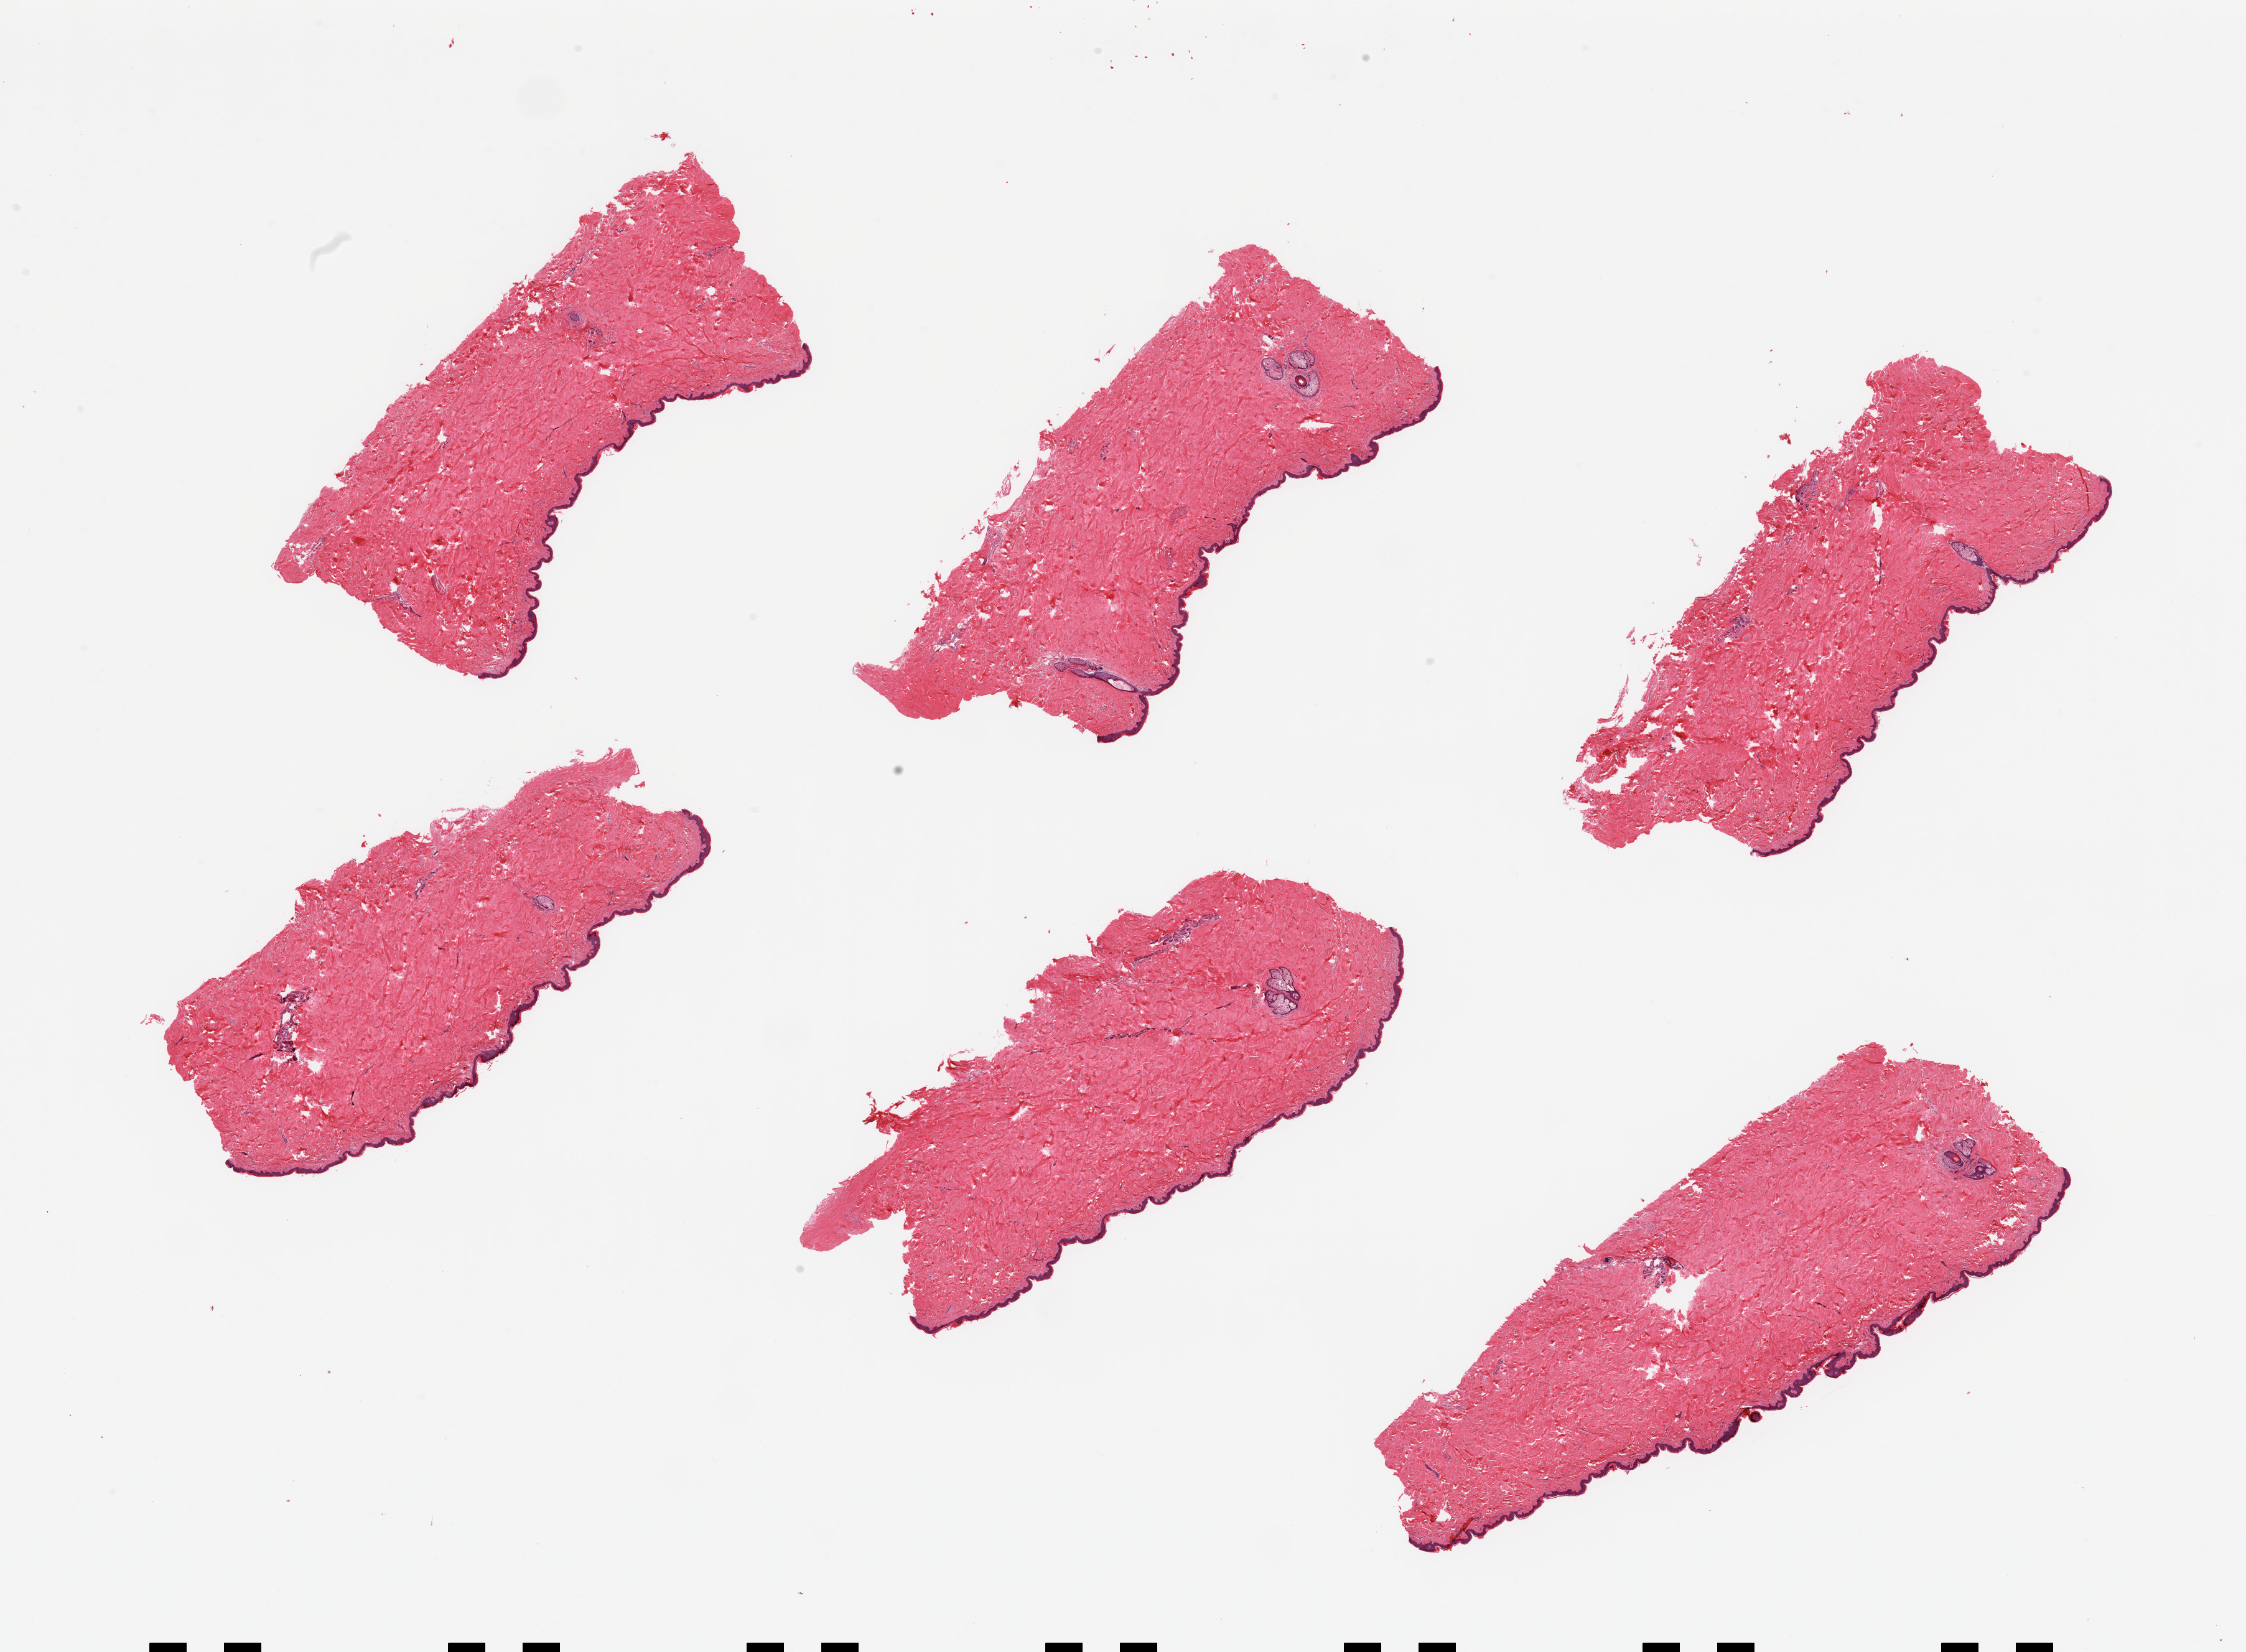
H&E whole-slide image, shown as a low-resolution overview of the whole scanned area (about 28.5 x 21.0 mm), PAXgene-fixed paraffin-embedded (PFPE) section, section of skin of suprapubic region (target tissue), donor tissue sample. Donor: male.
• reviewer comment on this tissue sample: 6 pieces, squamous epithelium is ~35-45 microns, no dermal fat